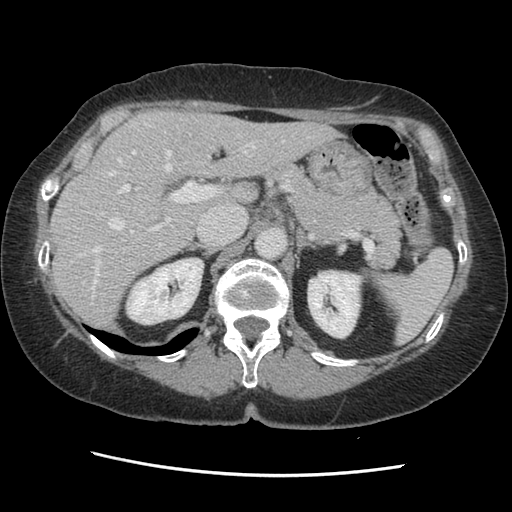
Contrast-enhanced abdominal CT, one axial slice. Slice 89 of 141 in the series (ordered by position). 120 kVp. Soft-tissue window (W 400 / L 40 HU). 512 × 512 image matrix. Female patient, age 61 years. Case-level facts recorded for this patient, not image findings: diagnosis: colorectal cancer liver metastases, imaged before liver resection; multiple liver metastases: no; largest metastasis: 2.4 cm; disease in both lobes: no.
Structures marked on this image (manually delineated by an expert):
- hepatic veins: bounding box (x1, y1, x2, y2) in pixels: (83, 123, 309, 296)
- liver: (51, 111, 337, 330)
- planned liver remnant (the part of the liver to remain after resection): (52, 111, 337, 331)
- portal vein (with intrahepatic branches): (118, 150, 219, 252)